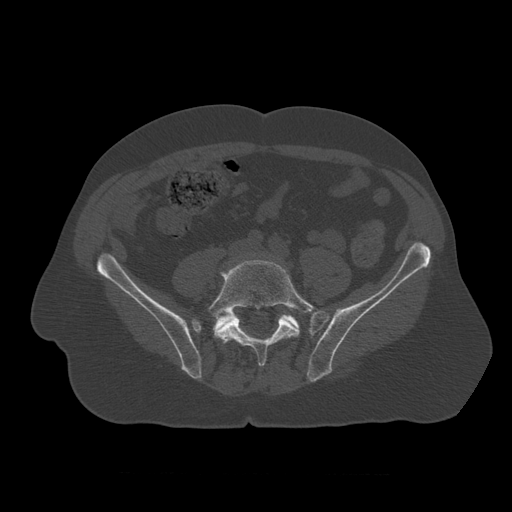
CT including the spine, one axial slice. Position 254 of 450 along the scan axis. Reconstruction kernel STANDARD. 120 kVp. Bone window (W 1800 / L 400 HU). 1.25 mm slice thickness. 512 × 512 image matrix. Patient age 75 years. Case-level facts recorded for this patient, not image findings: primary cancer: prostate.
Structures marked on this image (semi-automatically segmented with operator editing):
- L4 vertebra: bounding box [x1, y1, x2, y2] px = [254, 253, 256, 255]
- L5 vertebra: [207, 260, 319, 367]